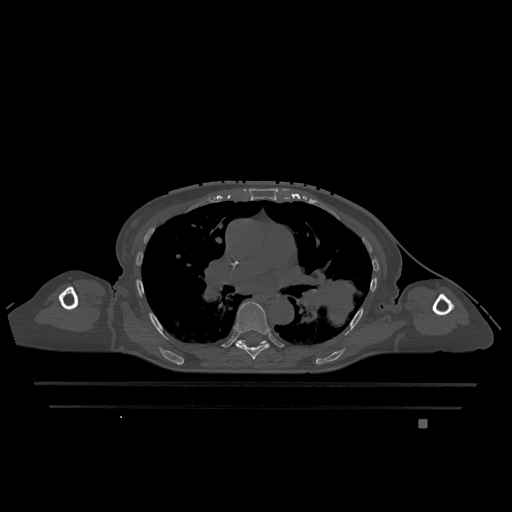
CT including the spine, one axial slice. Slice 777 of 1317 in the series (ordered by position). Bone window (W 1800 / L 400 HU). 0.5 mm slice thickness. 512 × 512 image matrix, field of view 500 × 500 mm. Patient: female, 74 years. Case-level facts recorded for this patient, not image findings: primary cancer: lung.
Annotated regions visible in this slice (semi-automatically segmented with operator editing):
- T6 vertebra: bounding box (x1, y1, x2, y2) in pixels: (235, 301, 270, 360)
- T7 vertebra: (237, 340, 268, 345)